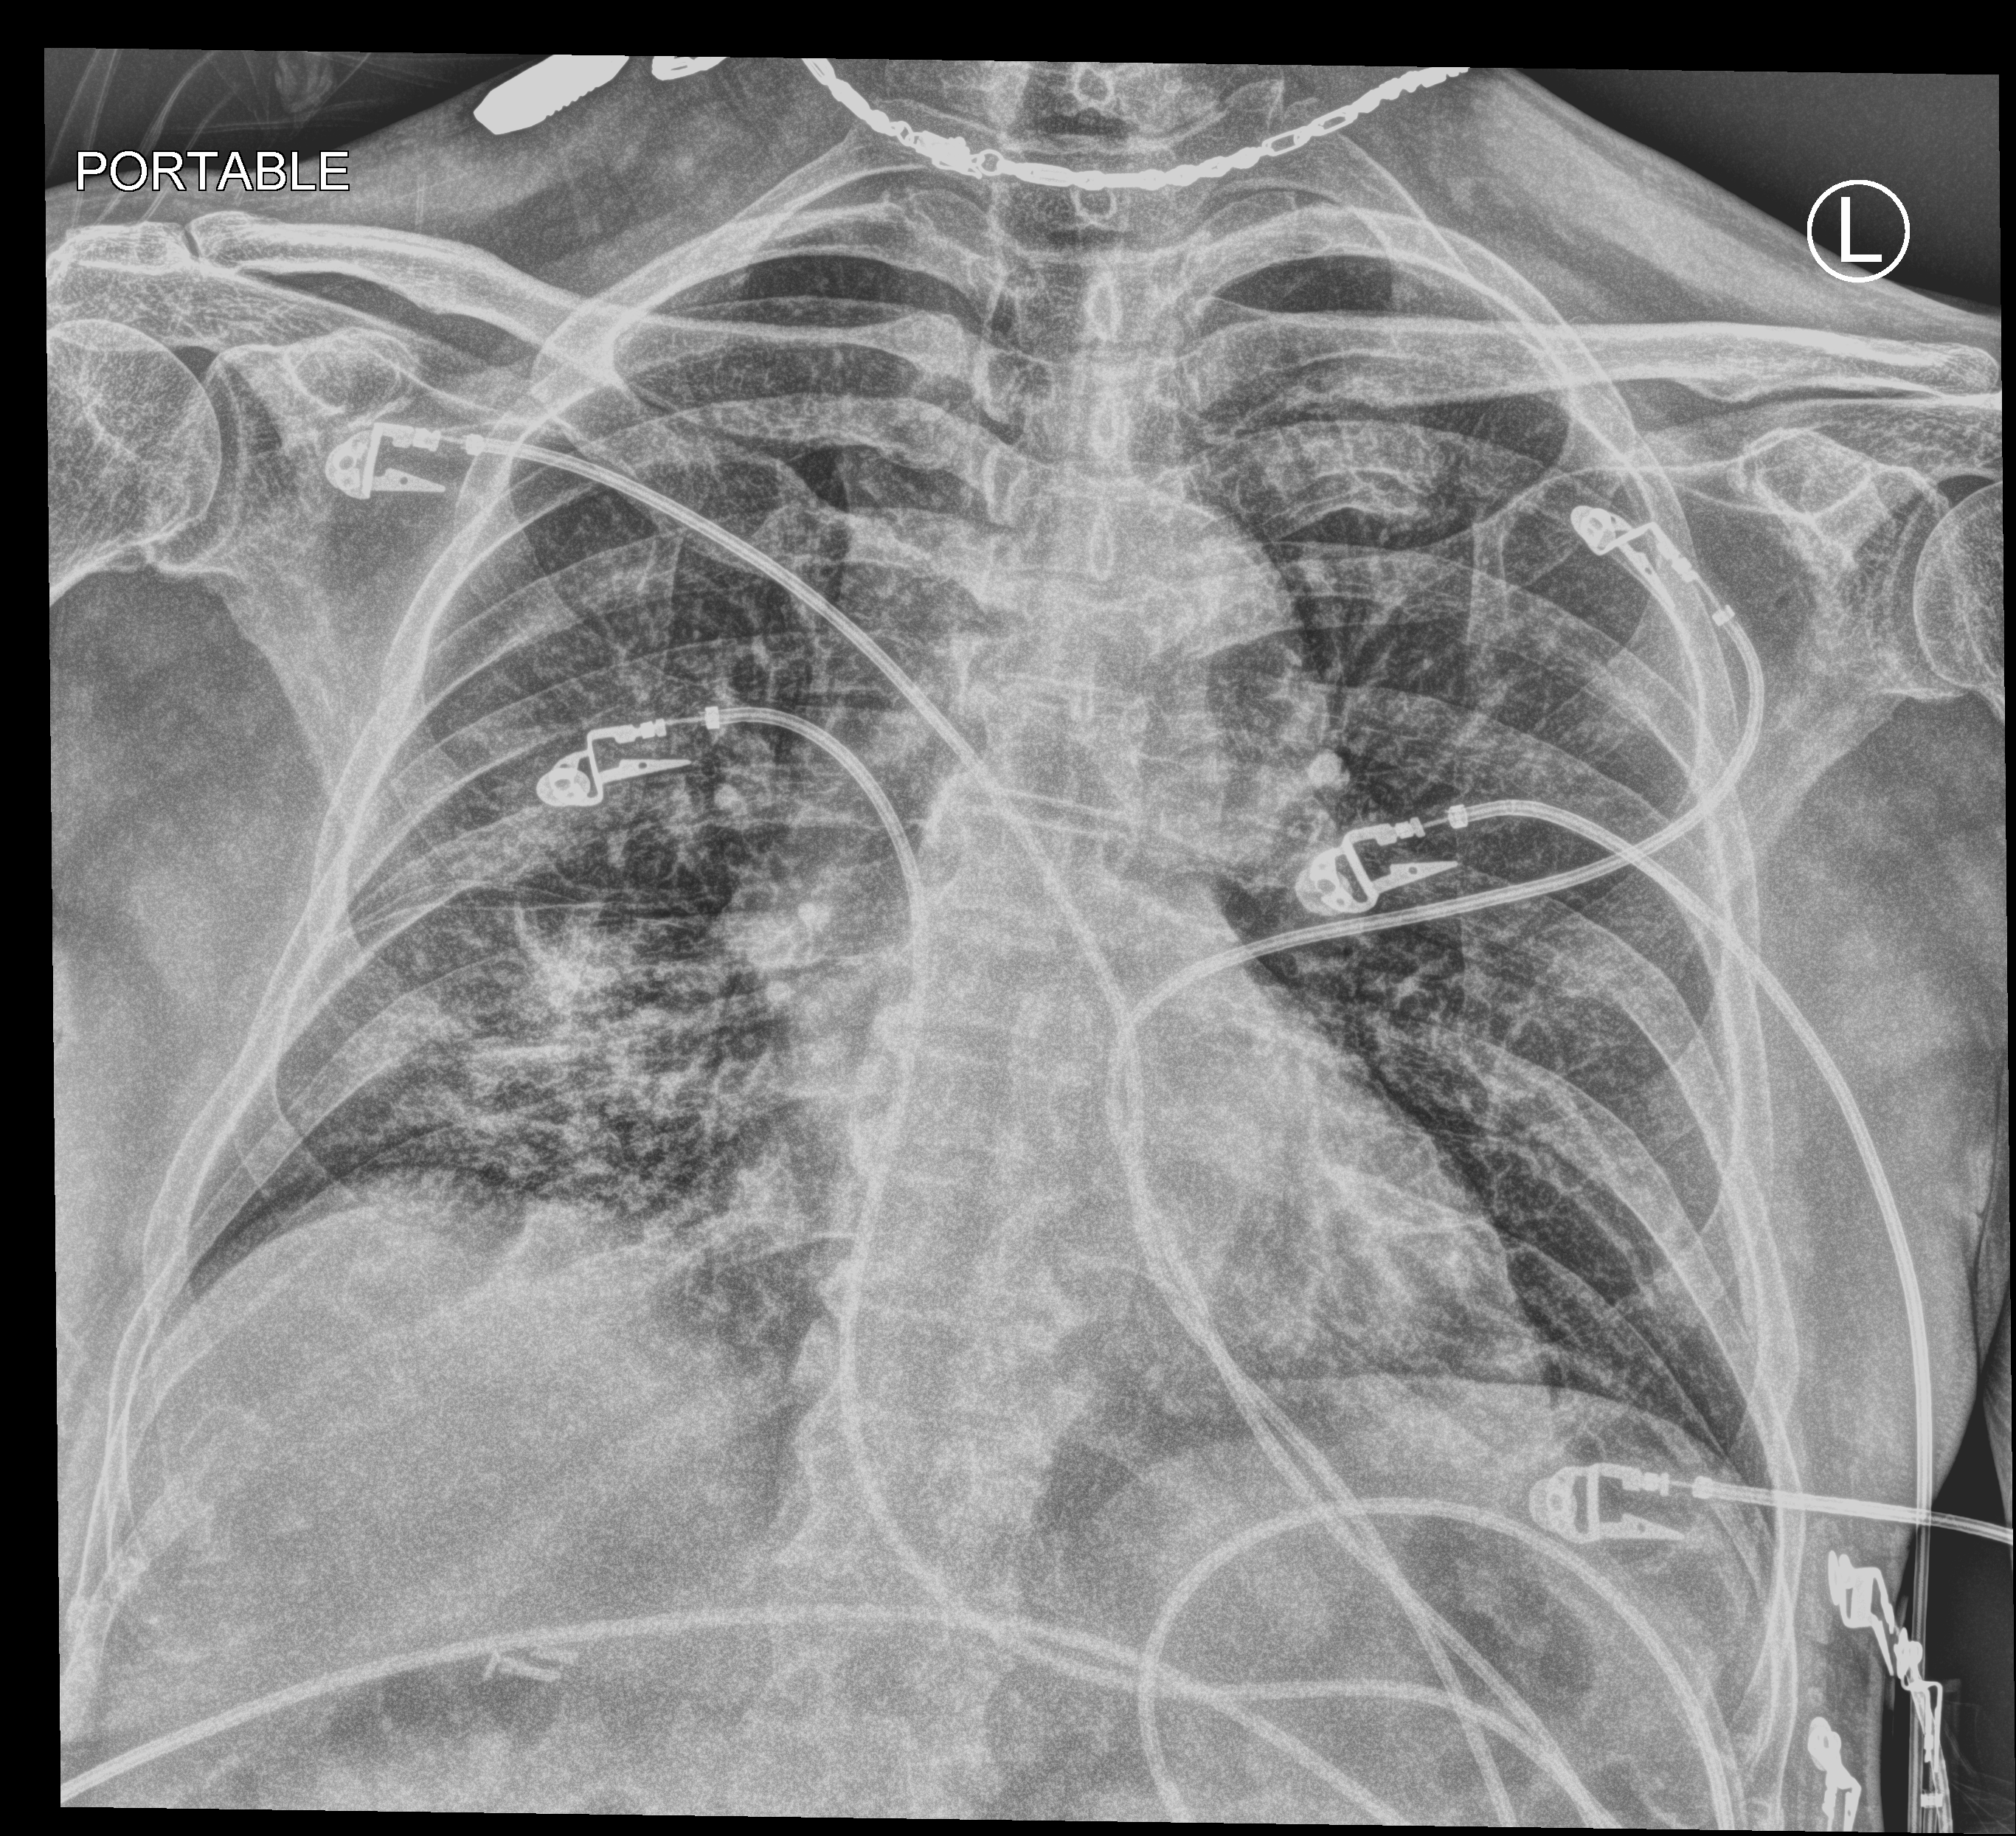
Chest X-ray (portable), anteroposterior (AP) projection. Patient hospitalised with COVID-19; male, aged 75–90 years.
Admission-level facts for this patient (not findings on this image; timing relative to this image not recorded):
- mechanically ventilated during this hospital stay: no